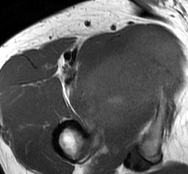
MRI of an extremity soft-tissue mass, one axial slice. Position 60 of 93 along the scan axis. MR volume resampled by the dataset authors to the PET/CT grid (not the native acquisition matrix). 188 × 174 image matrix, field of view 184 × 170 mm. Male patient. Case-level facts recorded for this patient, not image findings: histological type: undifferentiated - pleiomorphic; grade: high; site of the primary tumour: right thigh.
Outlined on this slice (expert contour drawn on MRI and transferred to this co-registered scan by the dataset authors):
- gross tumour volume including surrounding oedema: bounding box [x1, y1, x2, y2] px = [81, 28, 183, 130]
- gross tumour volume (mass): [81, 28, 183, 130]